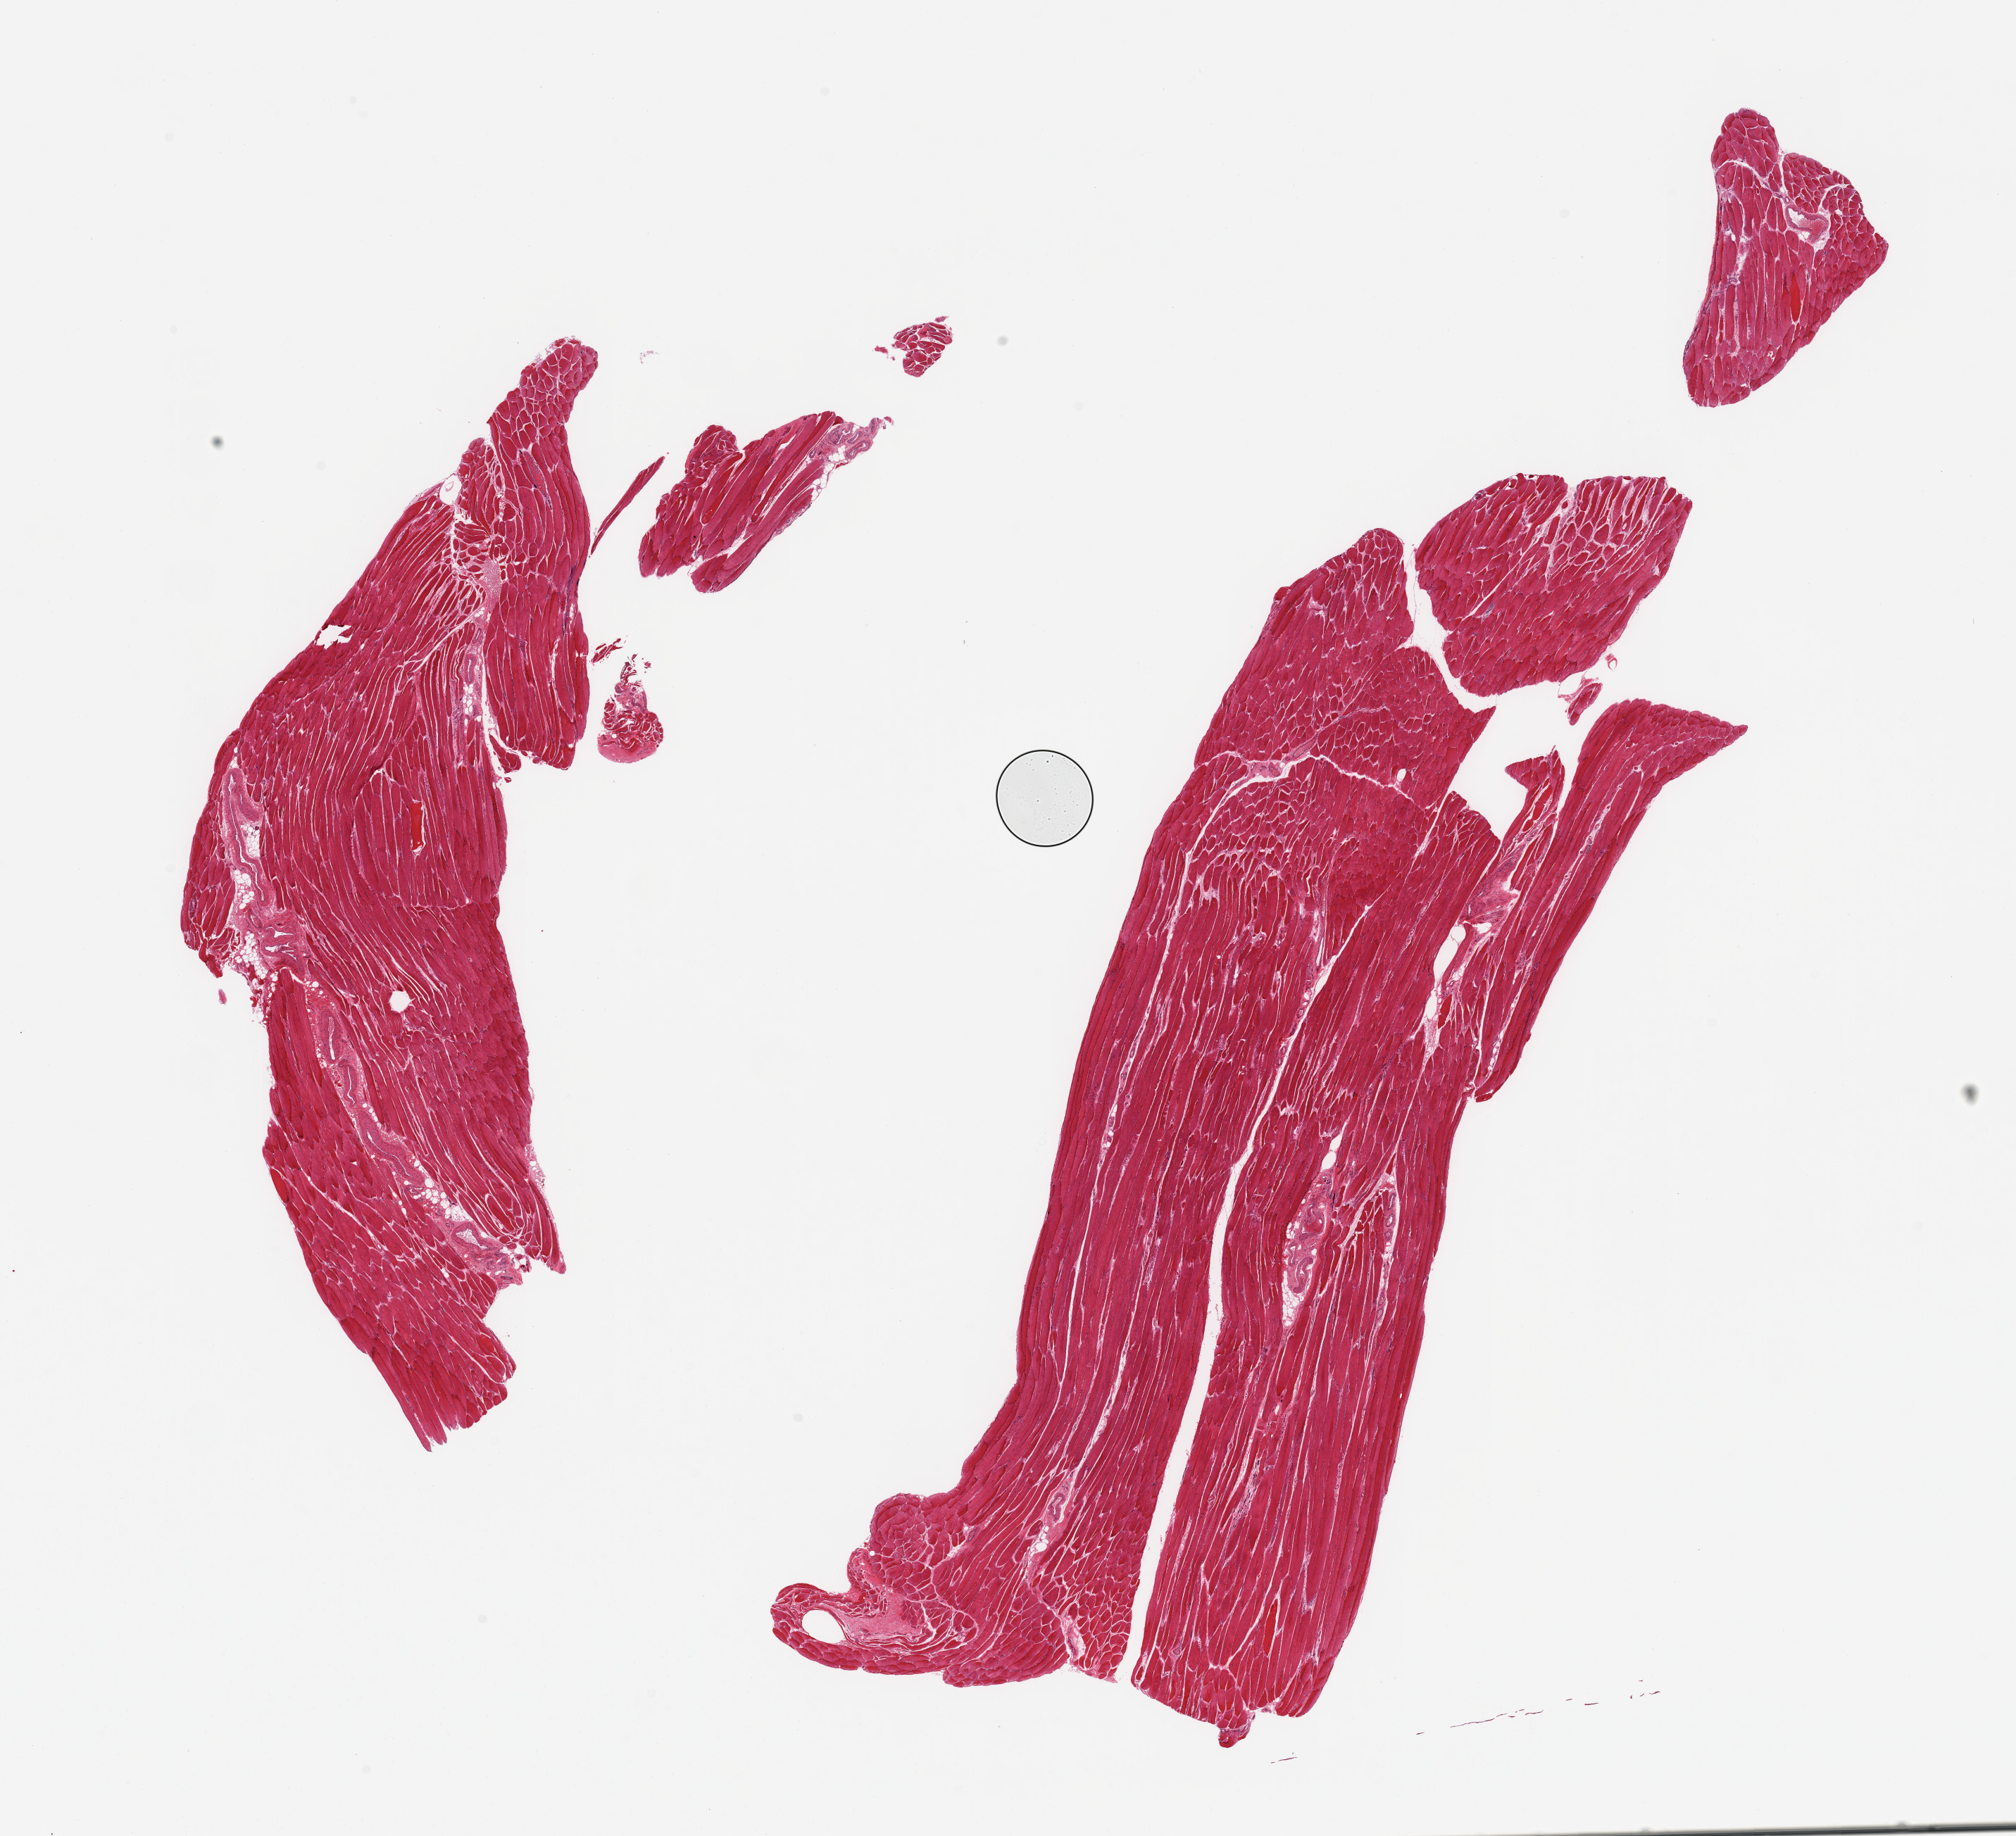
Digitized H&E-stained section, brightfield, shown as a low-resolution overview of the whole scanned area (about 22.6 x 20.6 mm, from a 20x scan); PAXgene-fixed paraffin-embedded (PFPE) section; section of skeletal muscle (target tissue); donor tissue sample.
Pathologist's review note for this sample: 2 pieces, trace interstitial fat.